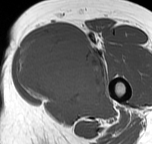
MRI of an extremity soft-tissue mass, one axial slice. Position 33 of 57 along the scan axis. MR volume resampled by the dataset authors to the PET/CT grid (not the native acquisition matrix). 3.27 mm slice thickness. 152 × 144 image matrix, field of view 148 × 141 mm. Female patient. Case-level facts recorded for this patient, not image findings: histological type: pleiomorphic leiomyosarcoma; grade: intermediate; site of the primary tumour: left thigh.
Outlined on this slice (expert contour drawn on MRI and transferred to this co-registered scan by the dataset authors):
- gross tumour volume including surrounding oedema: box from (x=16, y=37) to (x=105, y=105) px
- gross tumour volume (mass): (x=16, y=37)–(x=105, y=104)